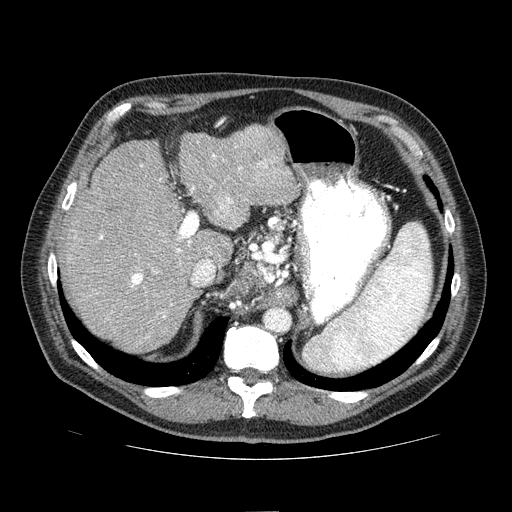
Contrast-enhanced abdominal CT (liver protocol), one axial slice; position 51 of 81 along the scan axis; reconstruction kernel STANDARD; 100 kVp; one of 2 acquisitions stored at this slice position; soft-tissue window (W 400 / L 40 HU); 2.5 mm slice thickness; 512 × 512 image matrix, field of view 400 × 400 mm. From the clinical record (not read from this slice): diagnosis: hepatocellular carcinoma (patient treated with transarterial chemoembolisation; whether this scan precedes or follows treatment is not stated here); TNM stage (as recorded): Stage-IIIA; Child-Pugh class: A; tumour differentiation: well differentiated; tumour size: 5.6 cm.
Annotated regions visible in this slice (semi-automatic segmentation, software-assisted and operator-edited):
- liver parenchyma outside the tumour (the mass and vessels are separate outlines, so this box may not span the whole liver): bounding box (x1, y1, x2, y2) in pixels: (60, 124, 298, 351)
- mass: (224, 125, 284, 178)
- liver vessels: (74, 141, 285, 338)